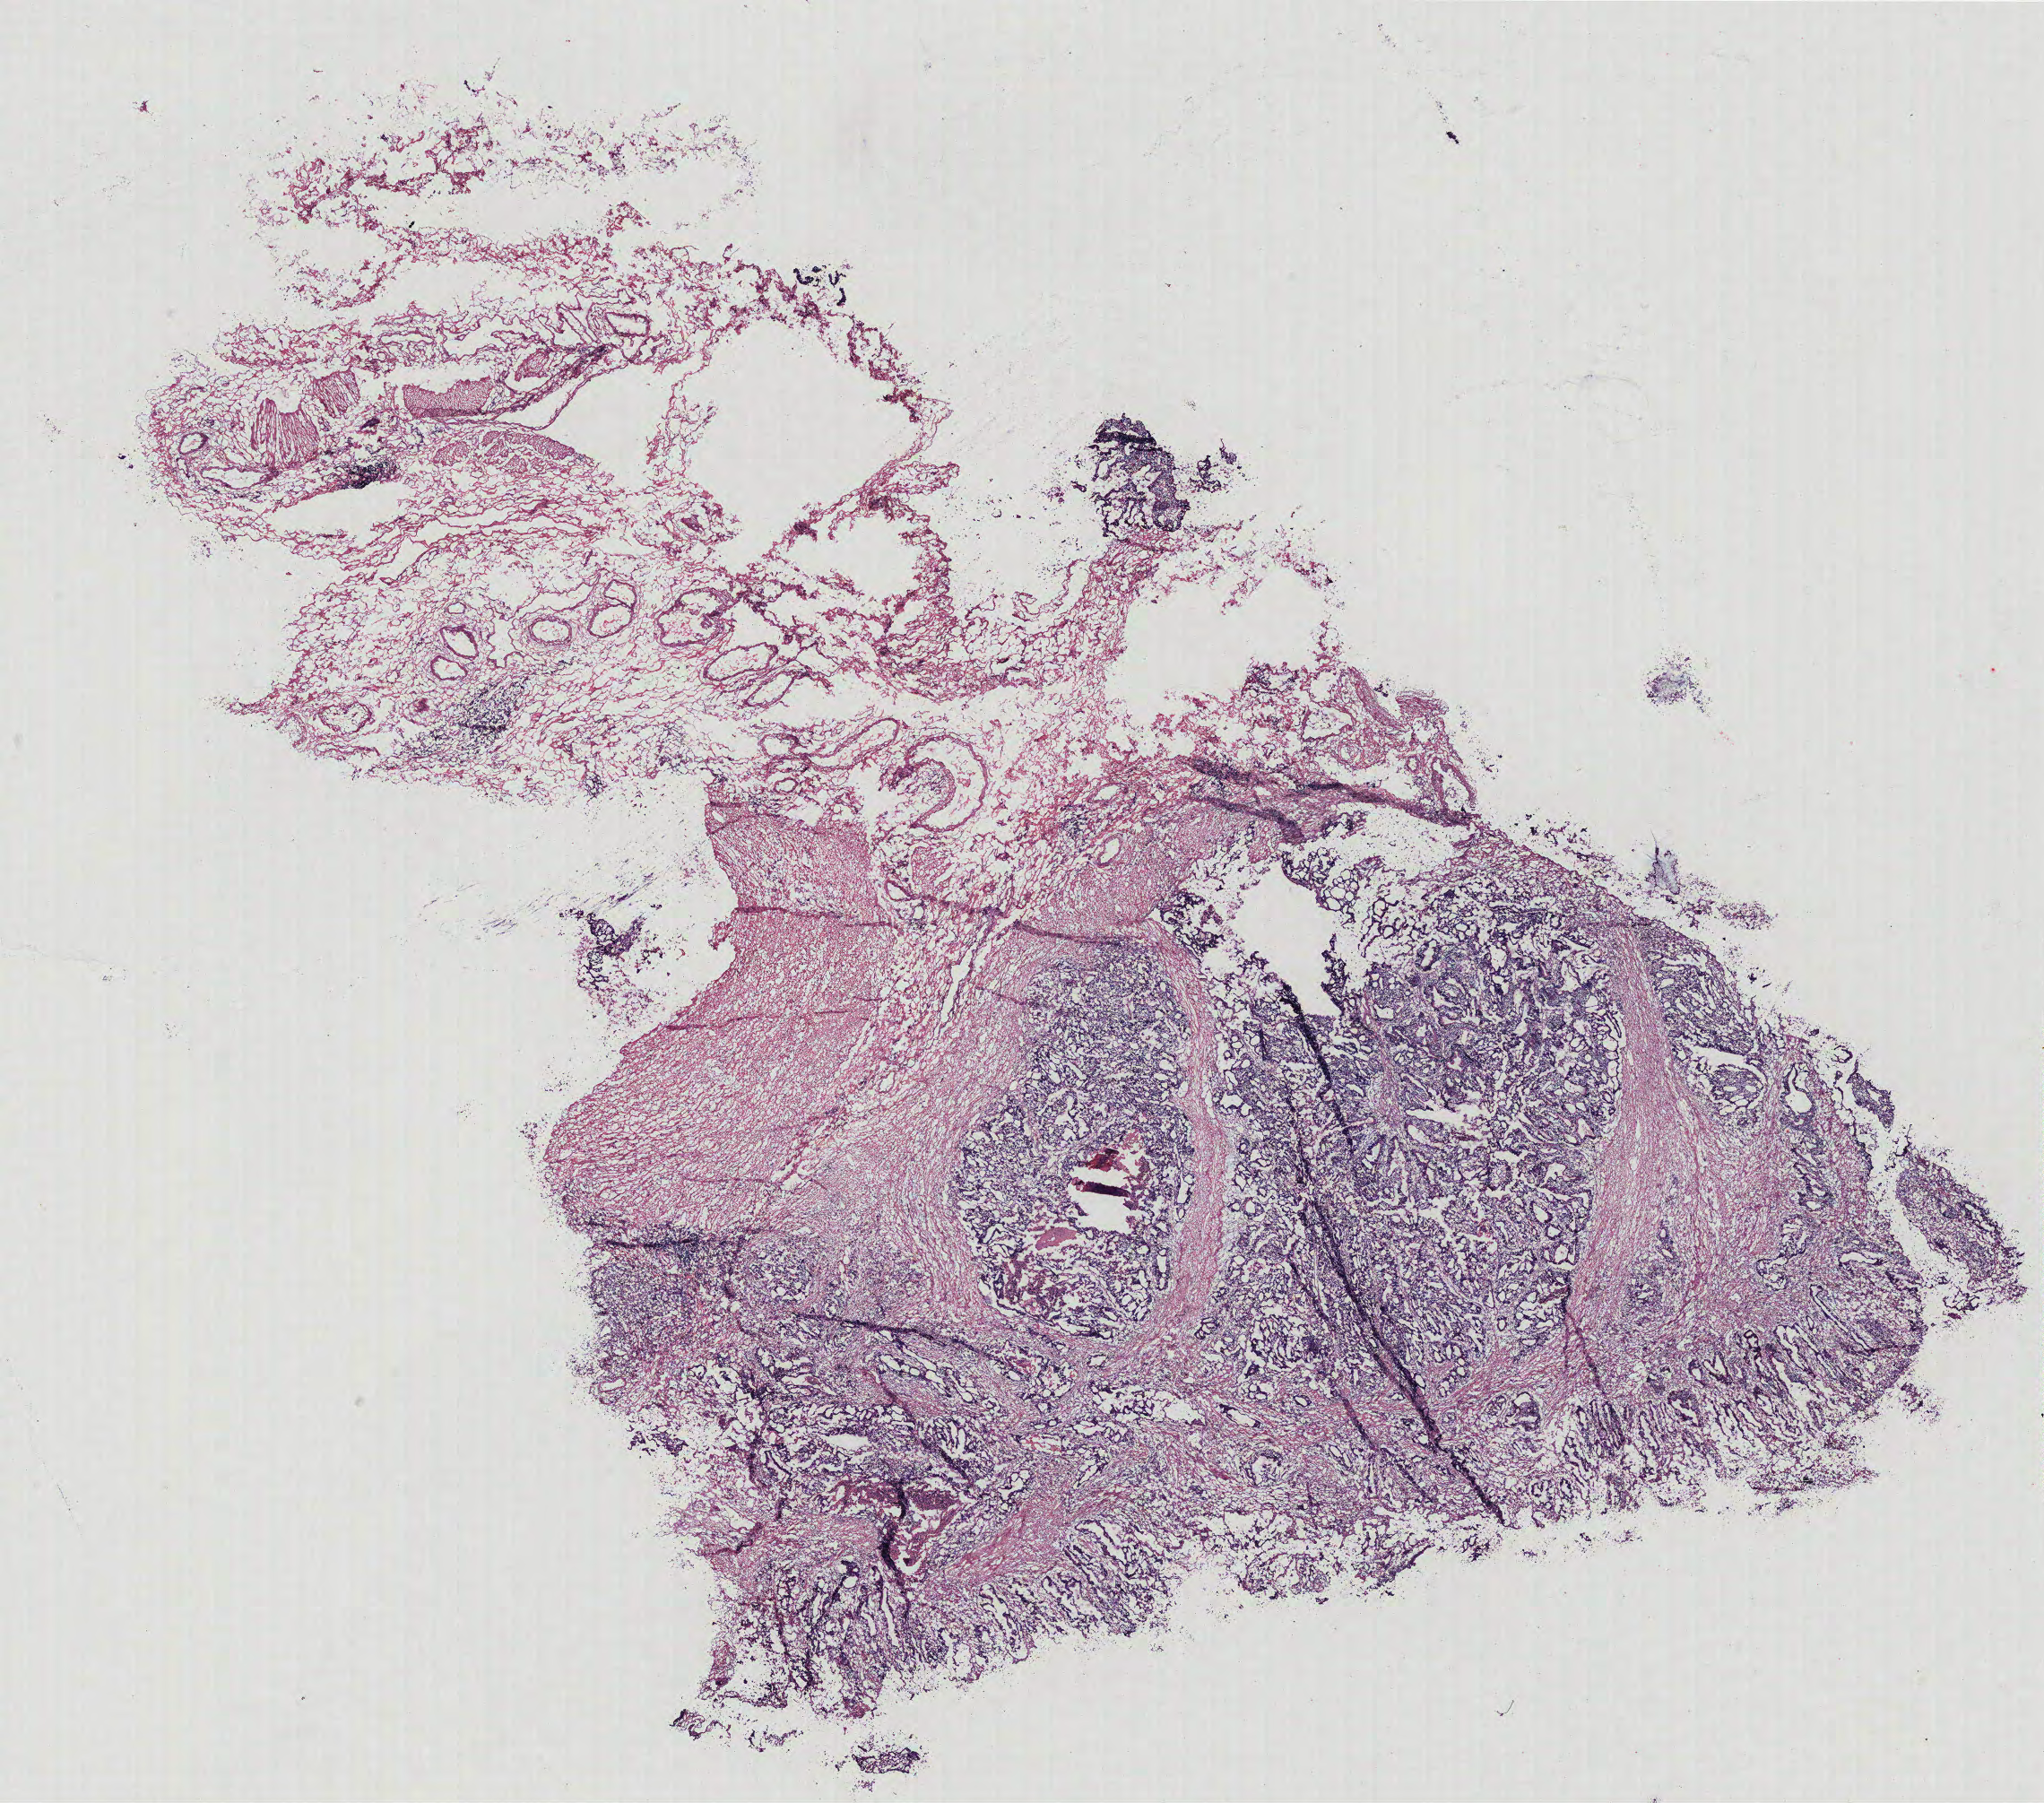
H&E whole-slide image — low-resolution overview of the scanned area, about 18.2 x 16.1 mm (from a 40x scan), tumour tissue sample, colon. Patient: female, age 52 years.
- primary tumour site (as recorded): colon
- diagnosis: Adenocarcinoma, NOS
- AJCC pathologic stage: IIIB